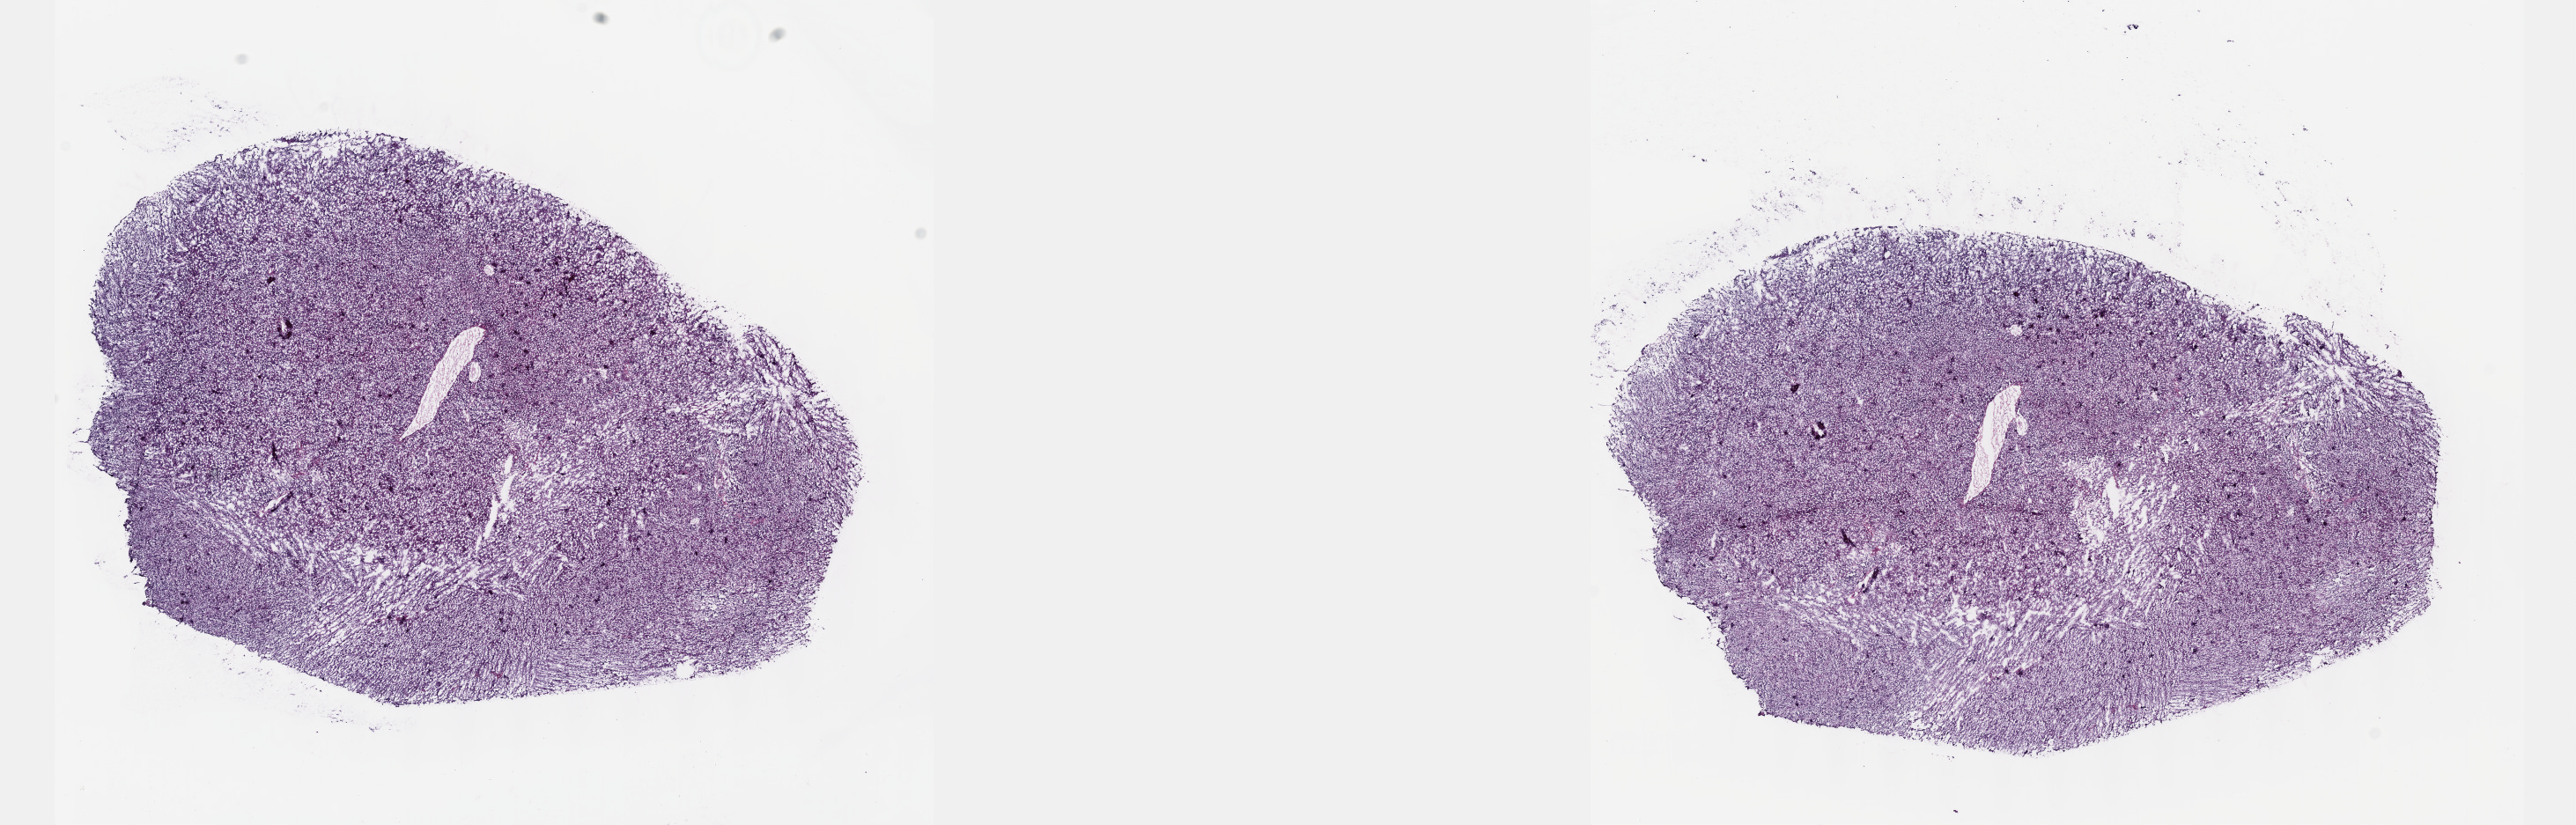
Whole-slide histology image, H&E-stained, shown as a low-resolution overview of the whole scanned area (about 23.6 x 7.6 mm, from a 40x scan), frozen section from the top of the tissue portion, primary tumour sample from the brain. Male patient; age at initial diagnosis 40 years. Histologic grade: G3 (poorly differentiated). Composition of this section per pathologist review: tumour cells 70%, tumour nuclei 85%, normal cells 10%, stromal cells 20%, necrosis 0%. Infiltration values recorded for this section: lymphocyte infiltration 0%, monocyte infiltration 0%, neutrophil infiltration 0%.
• histologic diagnosis: Astrocytoma, anaplastic (cerebrum)
• laterality: left